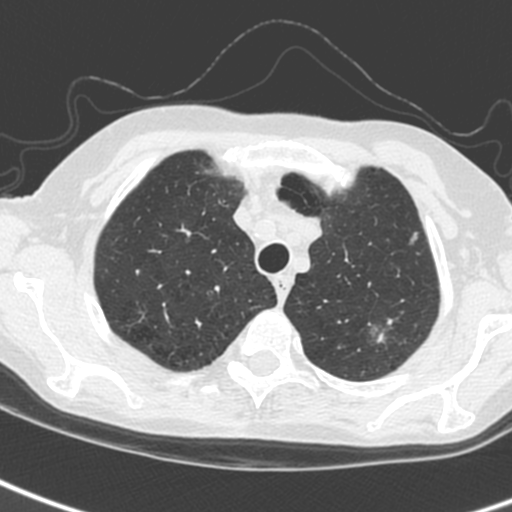
Low-dose screening chest CT, one axial slice; position 211 of 242 along the scan axis; 120 kVp; lung window (W 1500 / L -600 HU); 512 × 512 image matrix, field of view 284 × 284 mm.
Annotated regions visible in this slice (outlined manually by an expert reader):
- lesion 2 (tumor, upper lobe of left lung): bounding box [x1, y1, x2, y2] px = [411, 232, 418, 243]